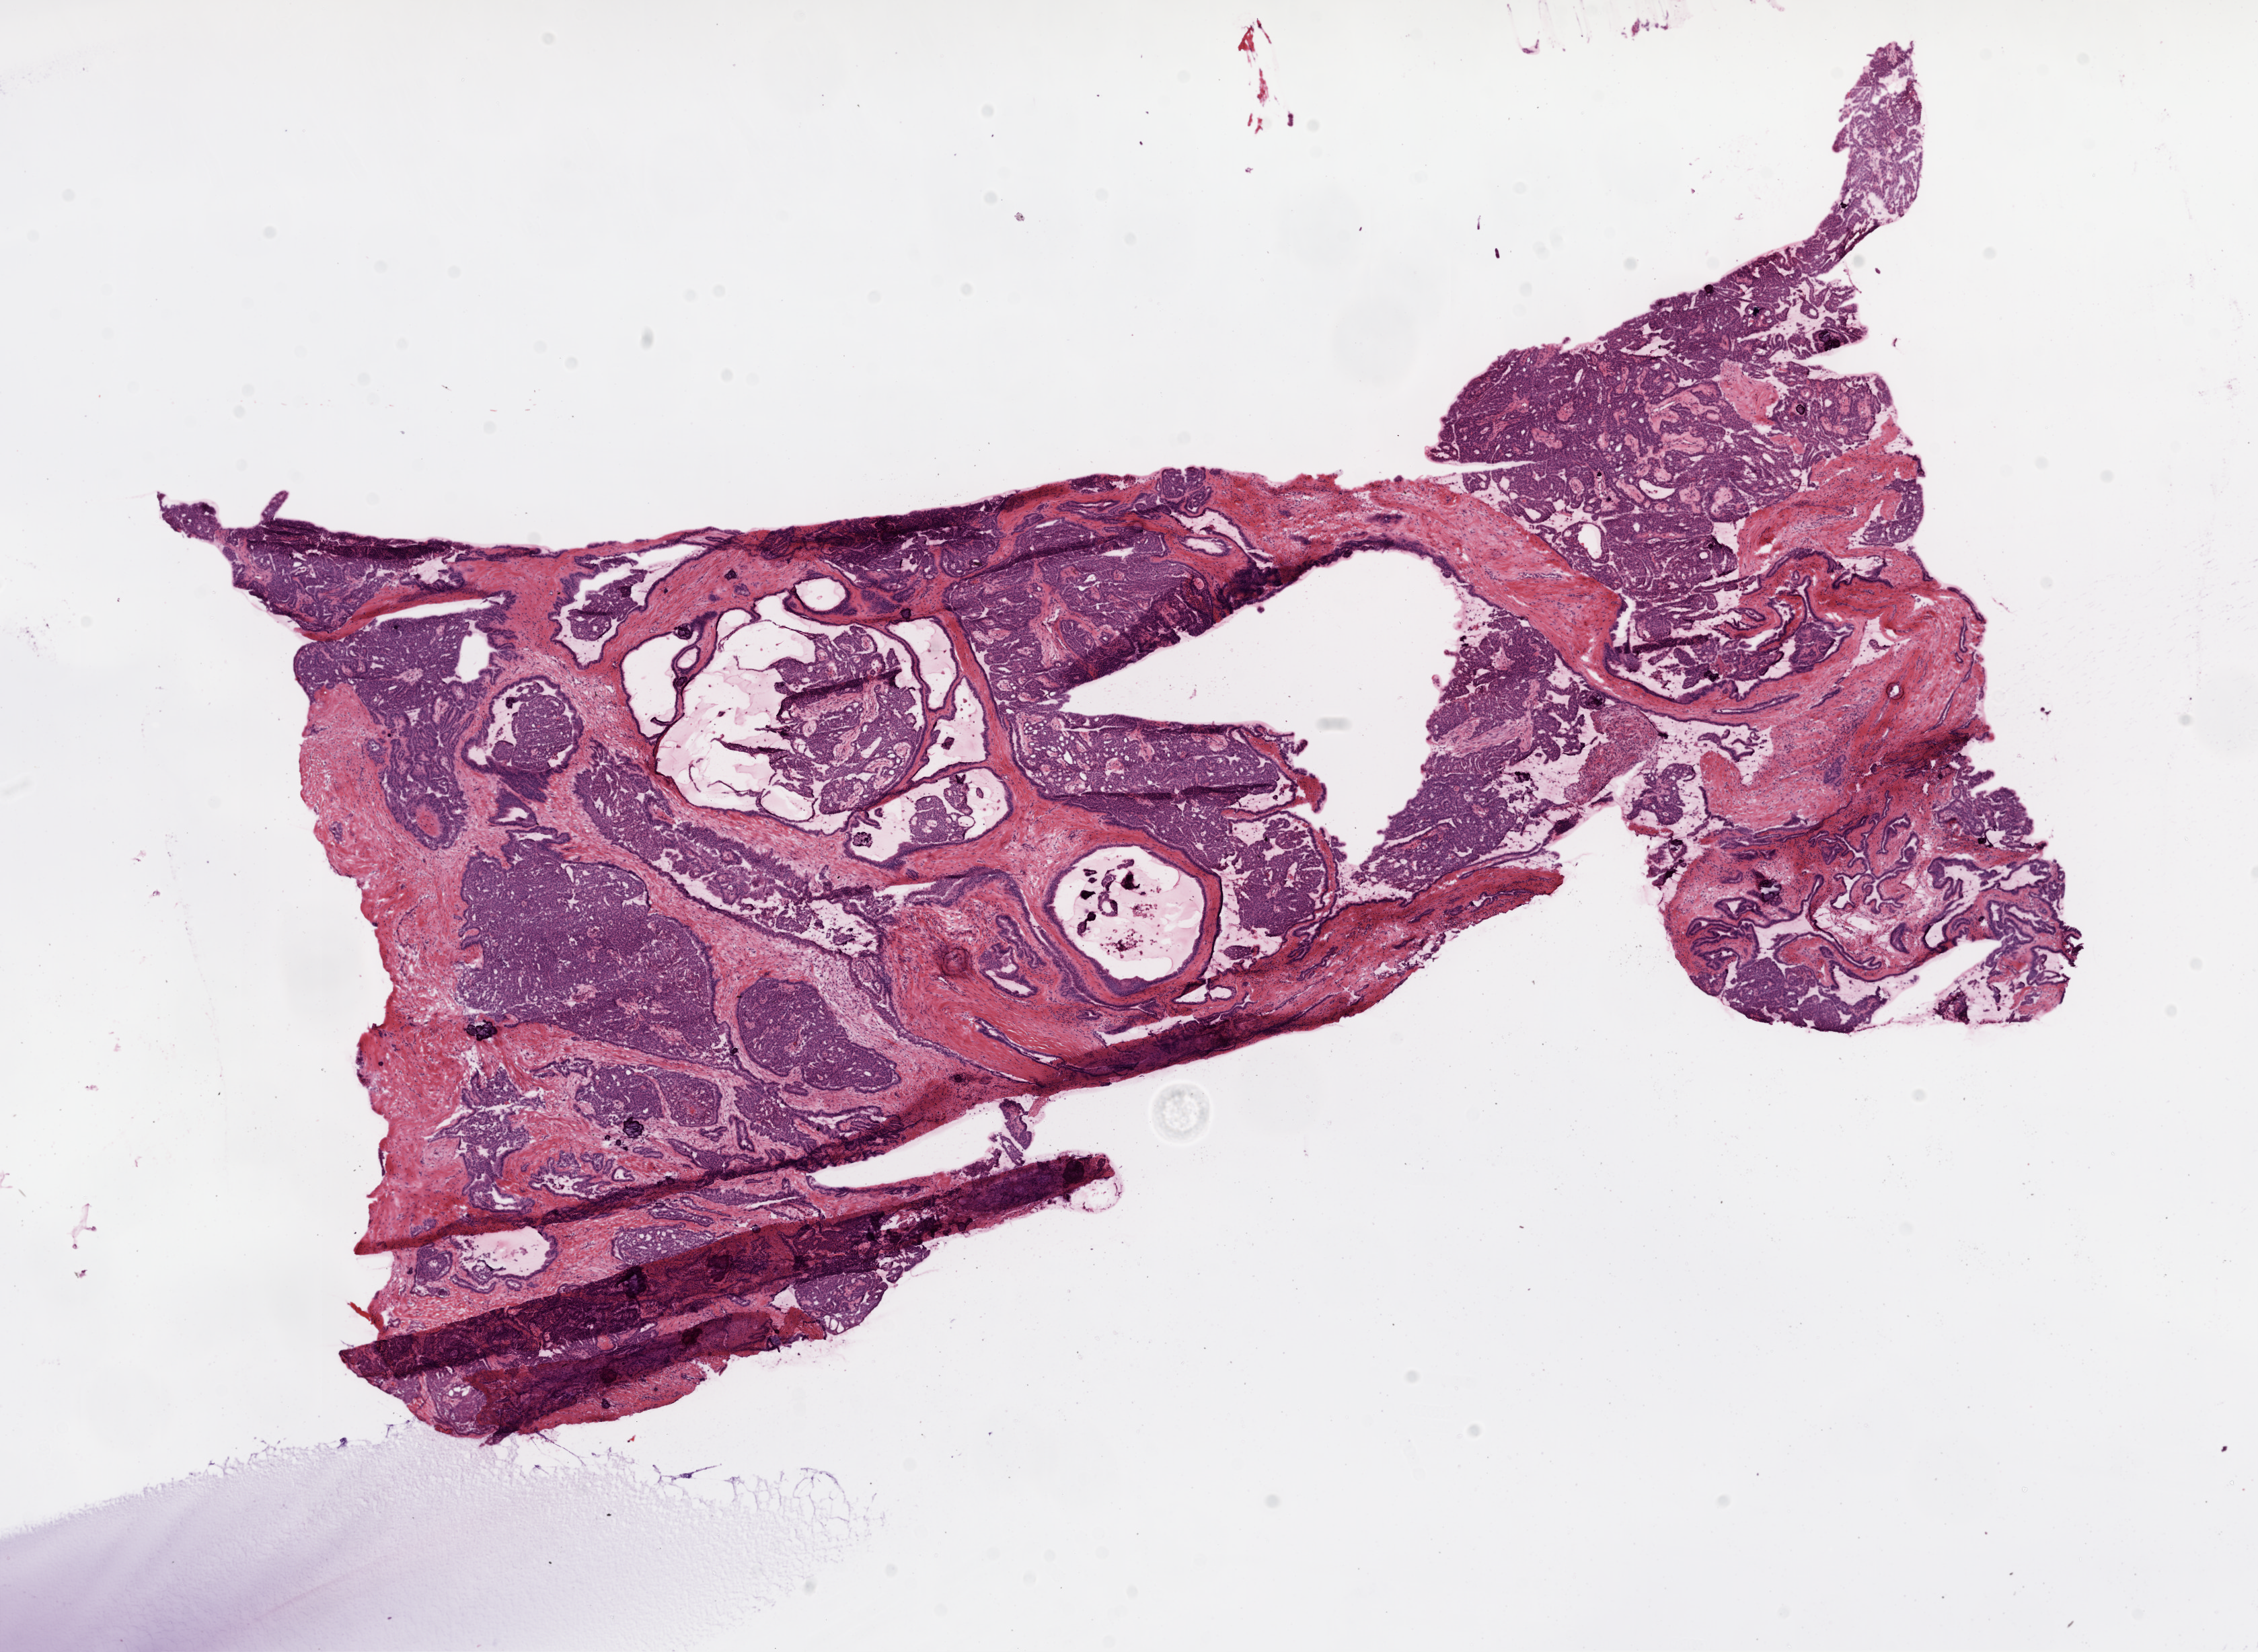
Whole-slide histology image, Hematoxylin and eosin (H&E) stained, whole scanned area (about 13.5 x 9.9 mm, from a 20x scan) shown as a low-resolution overview. Frozen section from the top of the tissue portion. Ovary, primary tumour sample. Patient: female, age at initial diagnosis 59 years. Histologic grade: G2 (moderately differentiated). Slide review estimates, as recorded: tumour cells 60%, tumour nuclei 70%, normal cells 18%, stromal cells 0%, necrosis 2%.
FIGO stage: IIIC. Diagnosis: Serous cystadenocarcinoma, NOS.